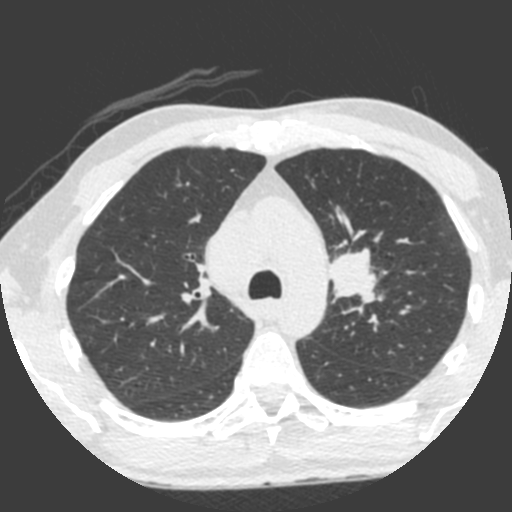
Low-dose screening chest CT, one axial slice; slice 153 of 212 in the series (ordered by position); lung window (W 1500 / L -600 HU); 2 mm slice thickness; 512 × 512 image matrix.
Outlined on this slice (expert manual segmentation):
- lesion 1 (tumor, upper lobe of left lung): box from (x=329, y=249) to (x=377, y=304) px